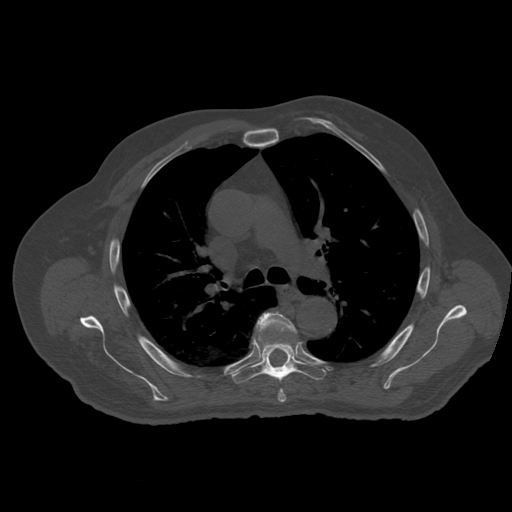
CT including the spine, one axial slice; slice 388 of 399 in the series (ordered by position); reconstruction kernel STANDARD; 120 kVp; bone window (W 1800 / L 400 HU); 1.25 mm slice thickness; 512 × 512 image matrix, field of view 407 × 407 mm. Patient age 73 years. Case-level facts recorded for this patient, not image findings: primary cancer: prostate.
Outlined on this slice (semi-automatic segmentation, software-assisted and operator-edited):
- T5 vertebra: box from (x=257, y=312) to (x=296, y=403) px
- T6 vertebra: (x=232, y=329)–(x=326, y=383)